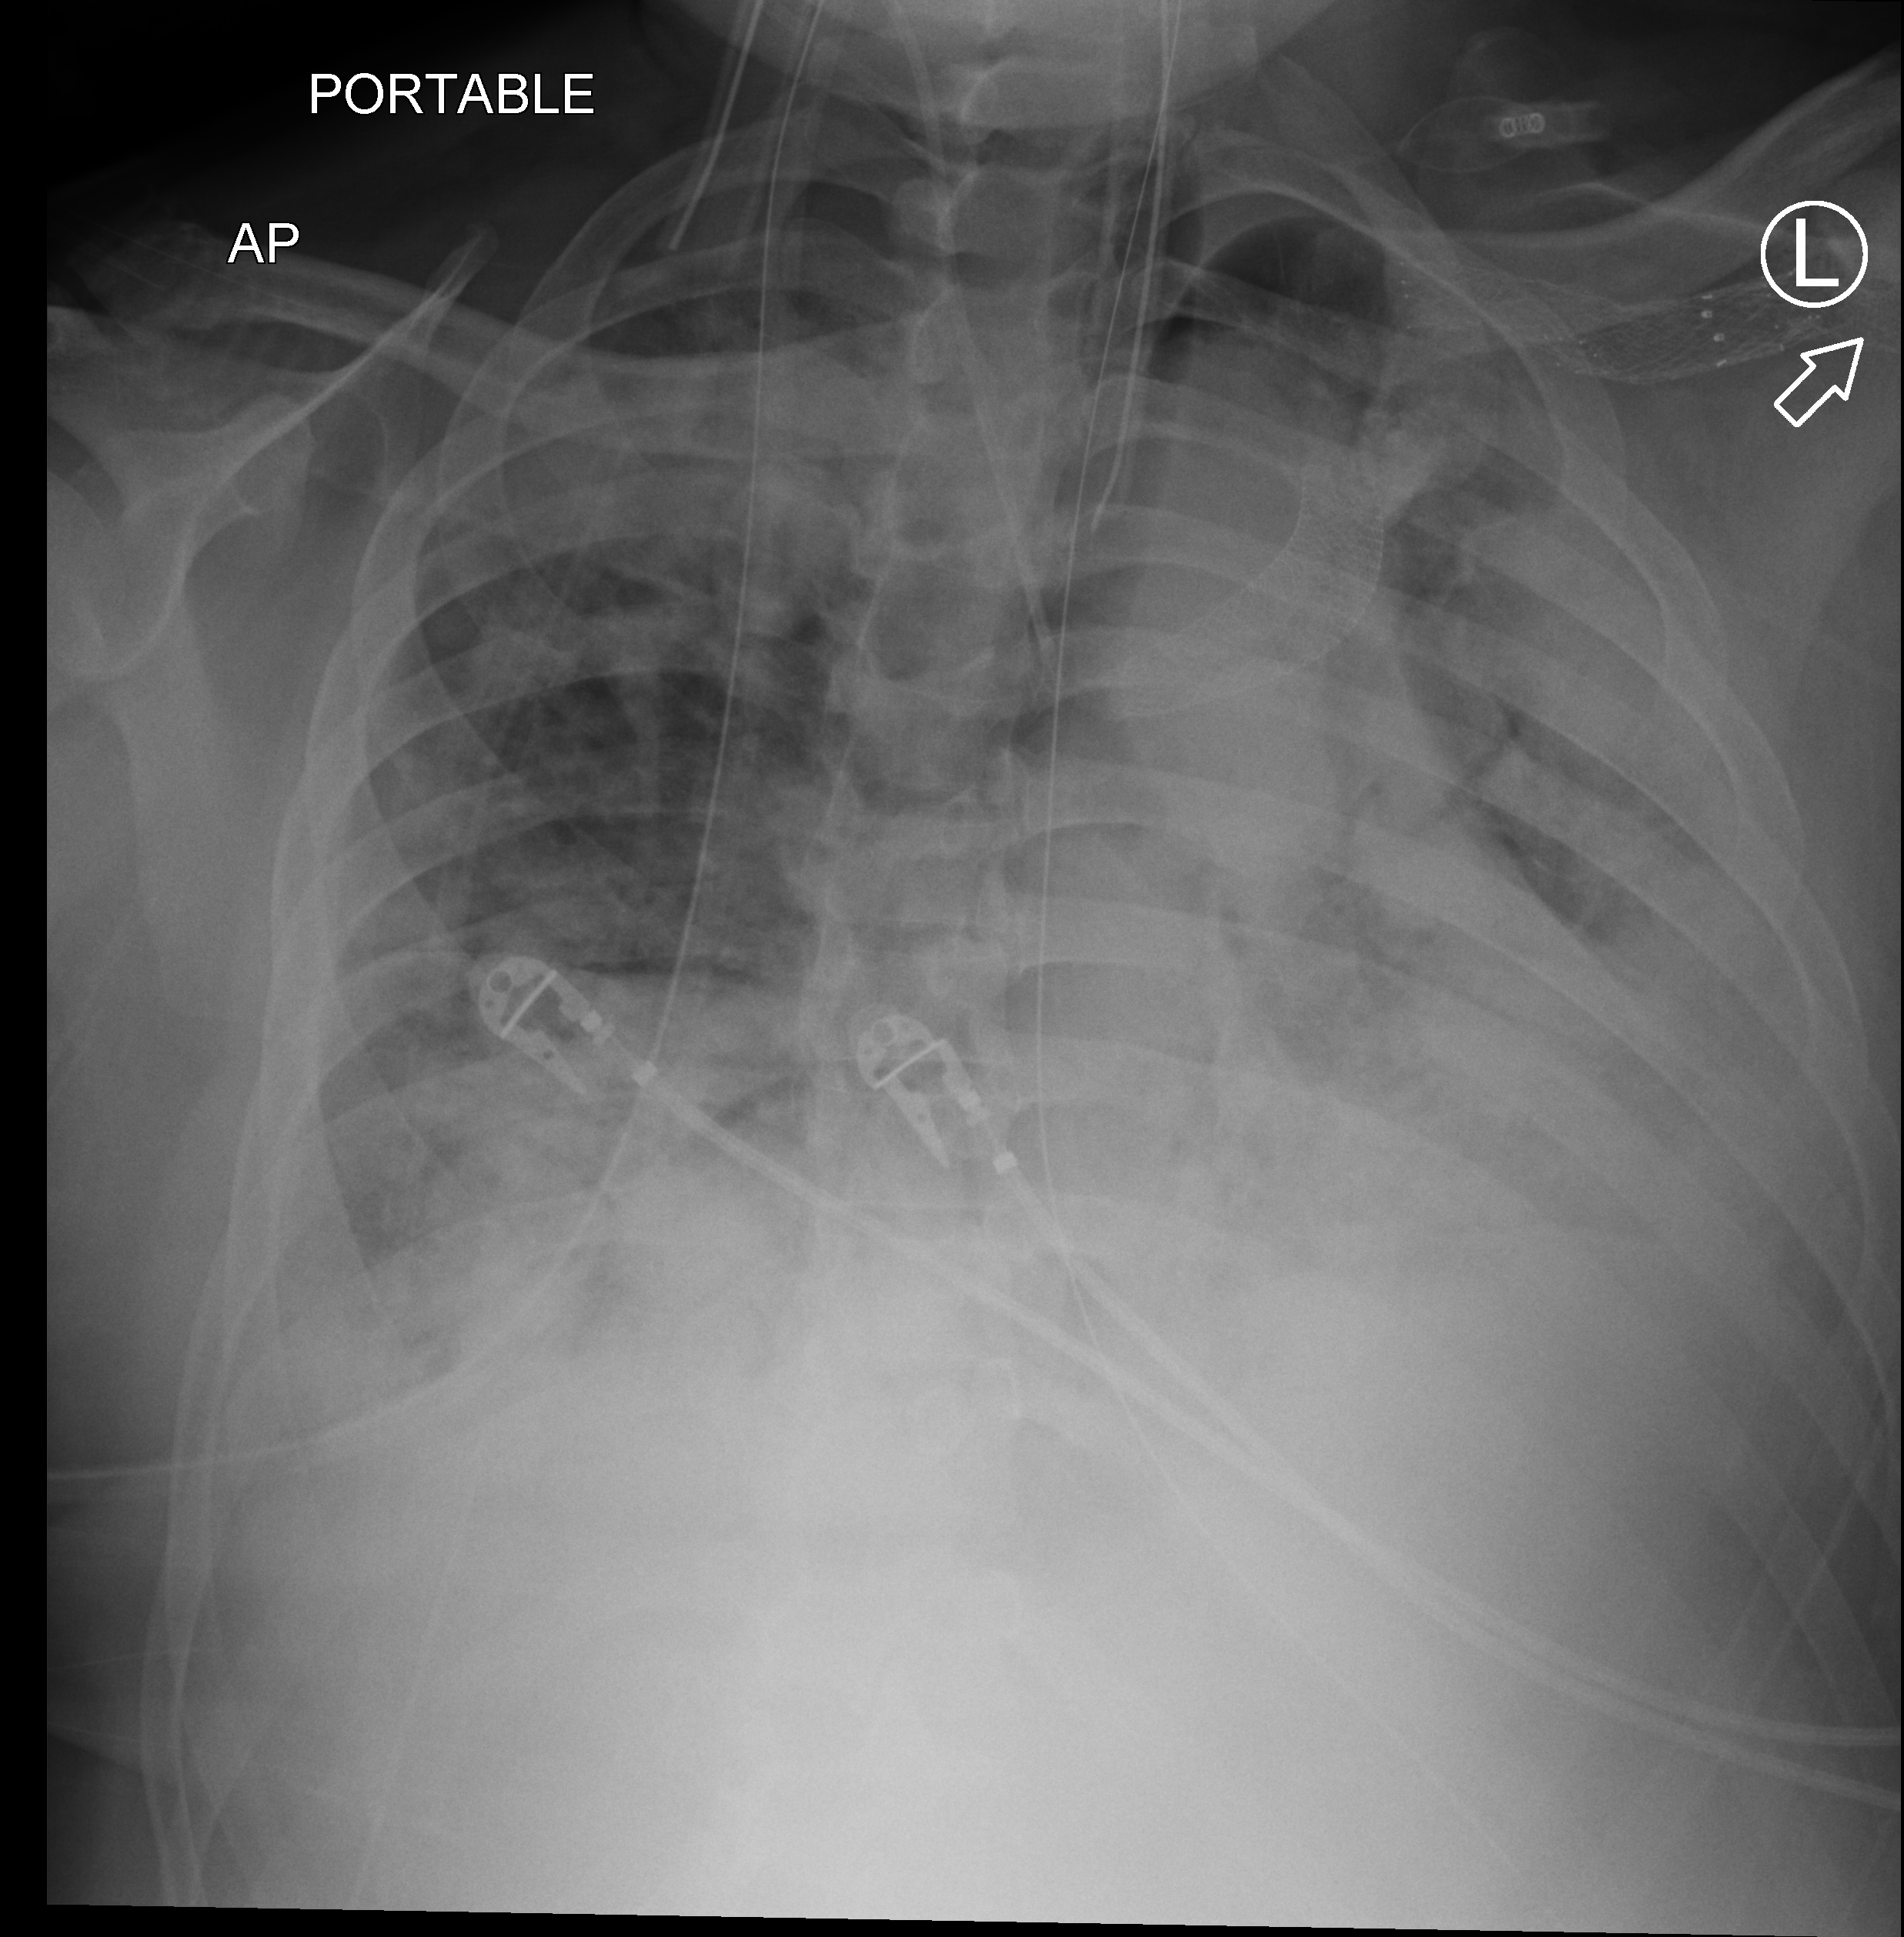
Bedside chest radiograph (computed radiography), anteroposterior (AP) projection. Male patient hospitalised with COVID-19, age 18–59 years.
From the hospital-stay record, not from the radiograph (when in the stay this image was taken is not recorded):
- mechanically ventilated during this hospital stay: yes